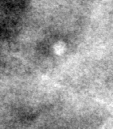
Crop from a digitized film mammogram around one marked abnormality; right breast; MLO view; BI-RADS breast density category 3 (scale 1–4).
Finding: calcifications, morphology lucent centered; BI-RADS assessment category 2; subtlety rating 3 on a 1 (subtle) to 5 (obvious) scale; benign; no additional work-up was recommended (benign without callback).